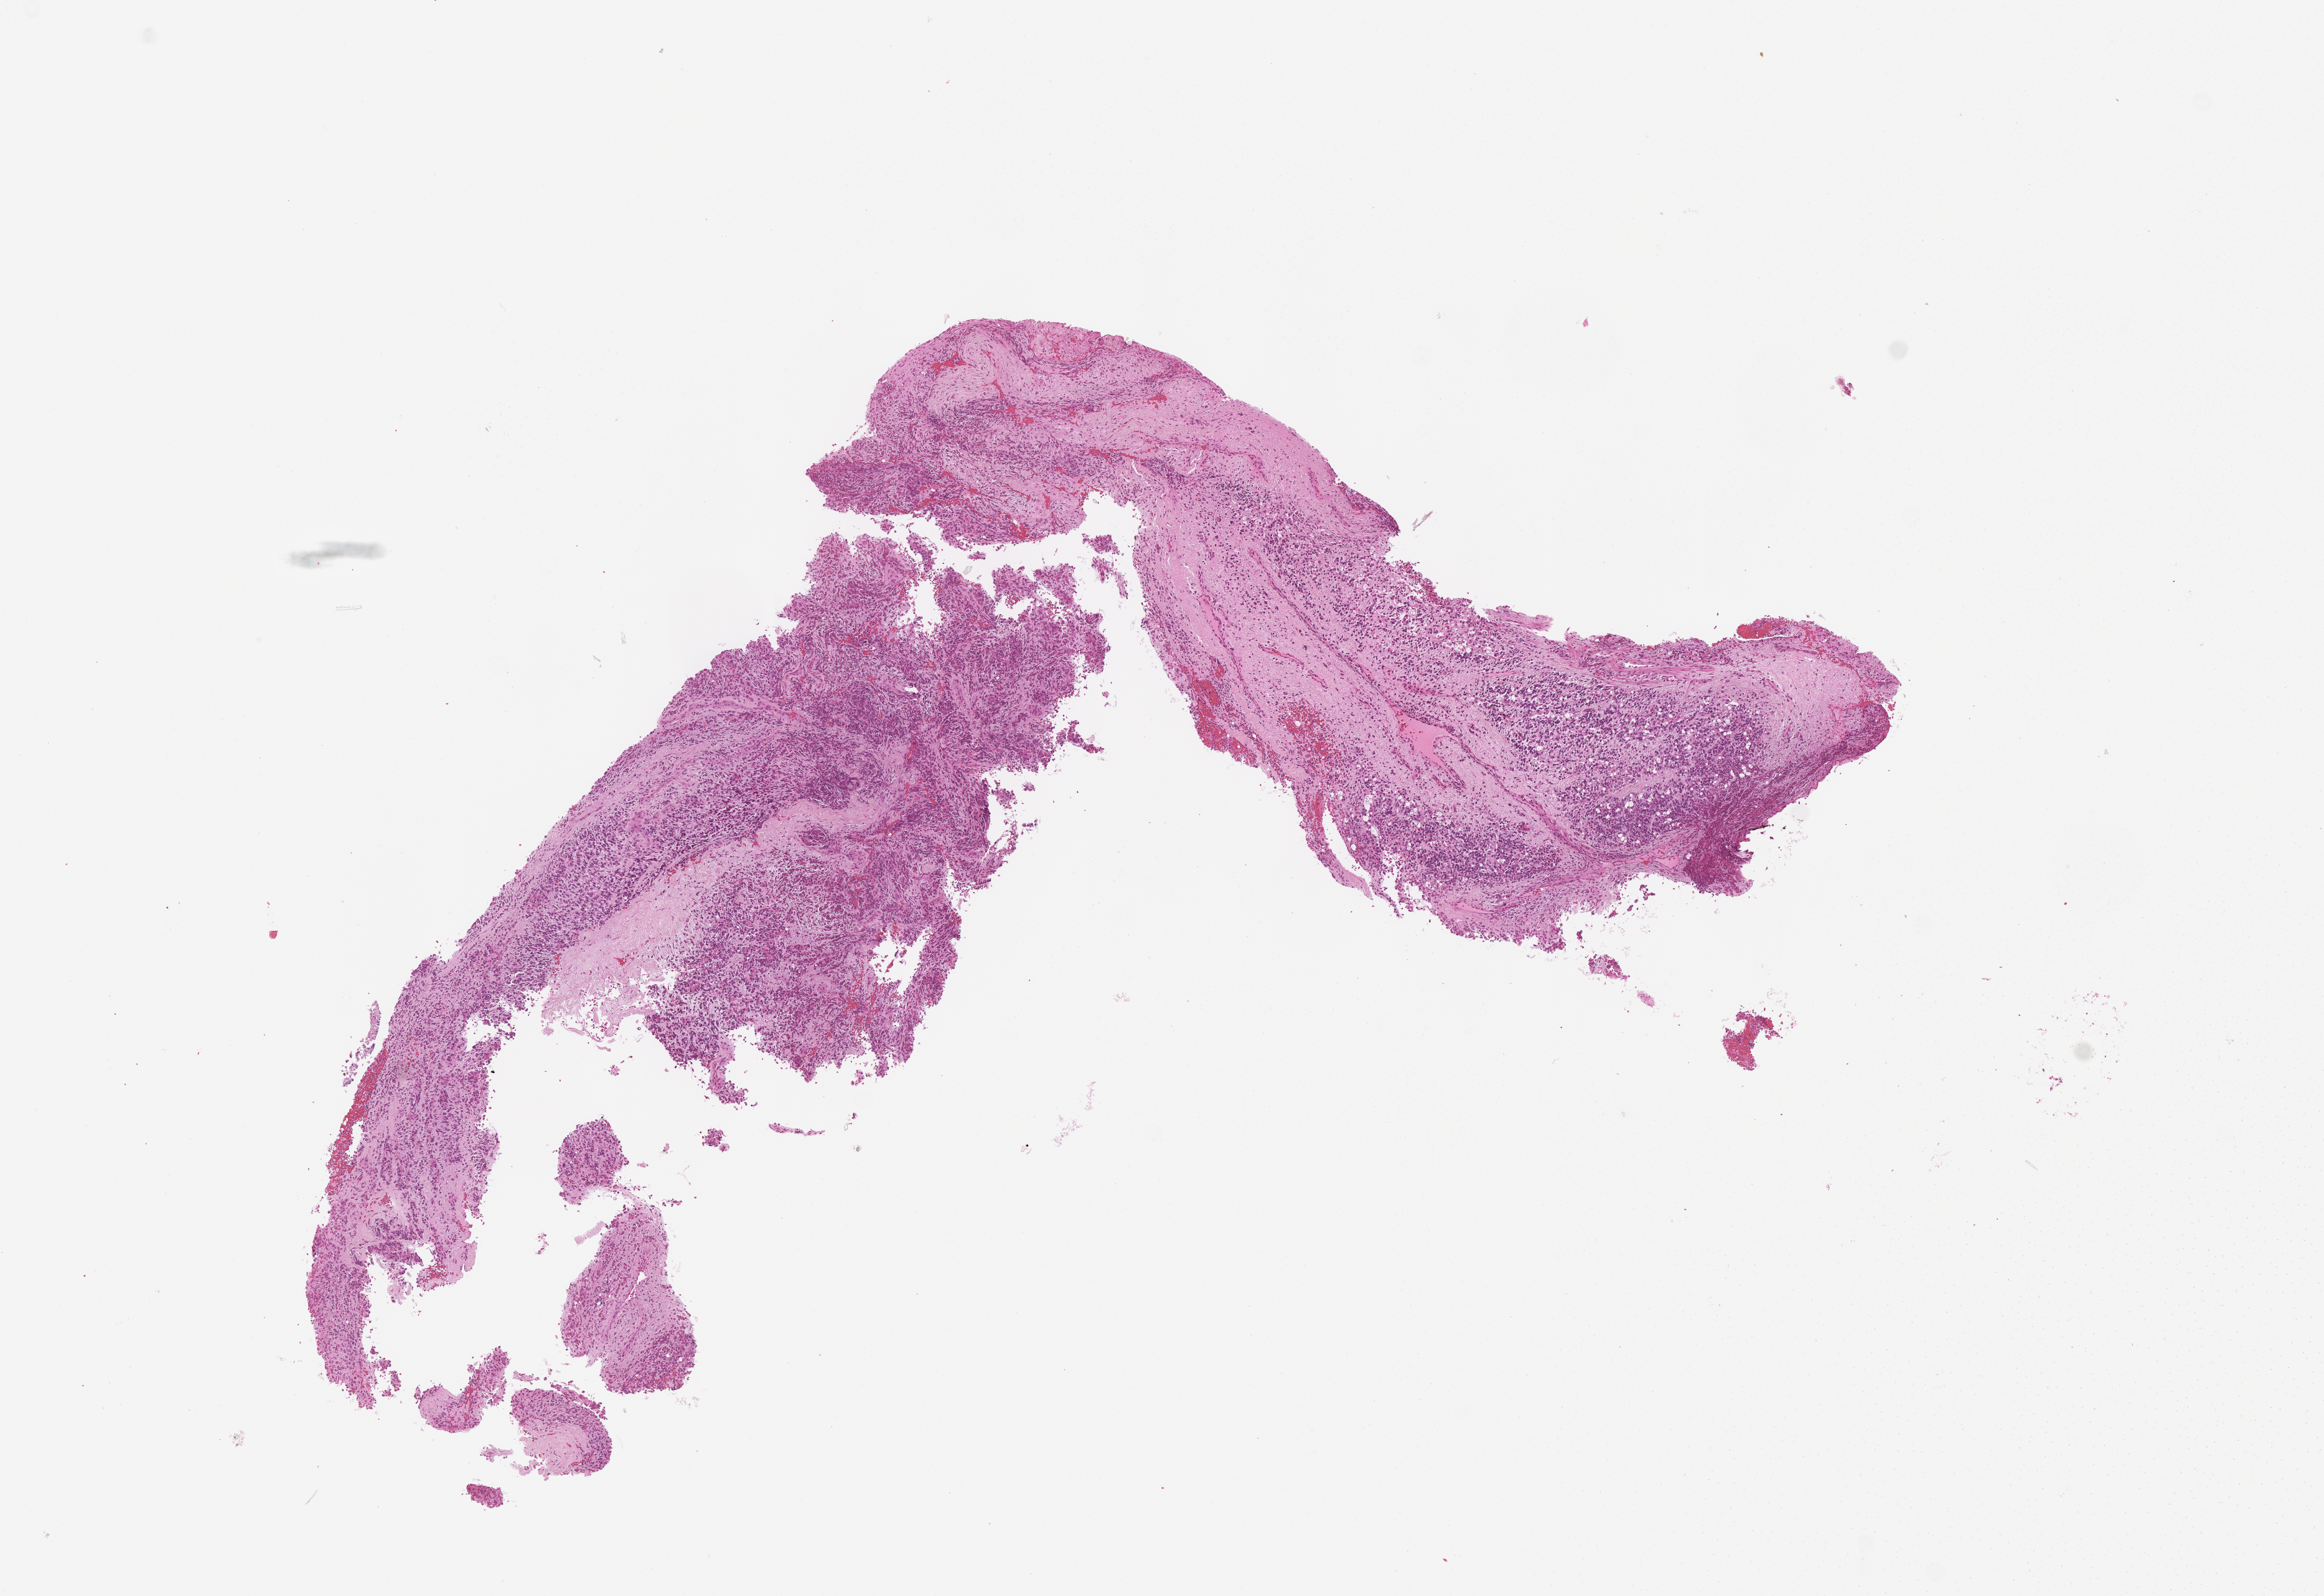
Whole-slide image, H&E stain of tumor tissue — whole scanned area (about 7.5 x 5.2 mm) shown as a low-resolution overview. FFPE section. Site: retroperitoneum. Patient: male, age 3.7 years at diagnosis.
* diagnosis: rhabdomyosarcoma; histological classification: embryonal rhabdomyosarcoma
* stage (as recorded): 3
* metastatic status at presentation (as recorded): non-metastatic (unconfirmed)